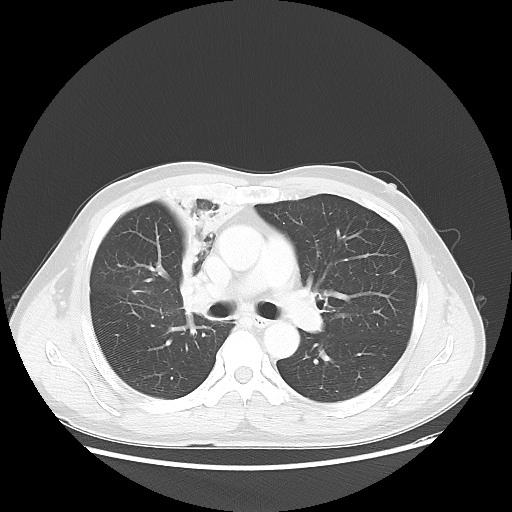
Chest CT, one axial slice. Position 33 of 56 along the scan axis. 100 kVp. Lung window (W 1500 / L -600 HU). 512 × 512 image matrix, field of view 398 × 398 mm. Male patient, age 60 years. From the clinical record (not read from this slice): clinical TNM (as recorded): T2a N1 M0.
Outlined on this slice (bounding box drawn by a radiologist):
- lung tumour (recorded histology: squamous cell carcinoma): bounding box [x1, y1, x2, y2] px = [157, 188, 248, 297]